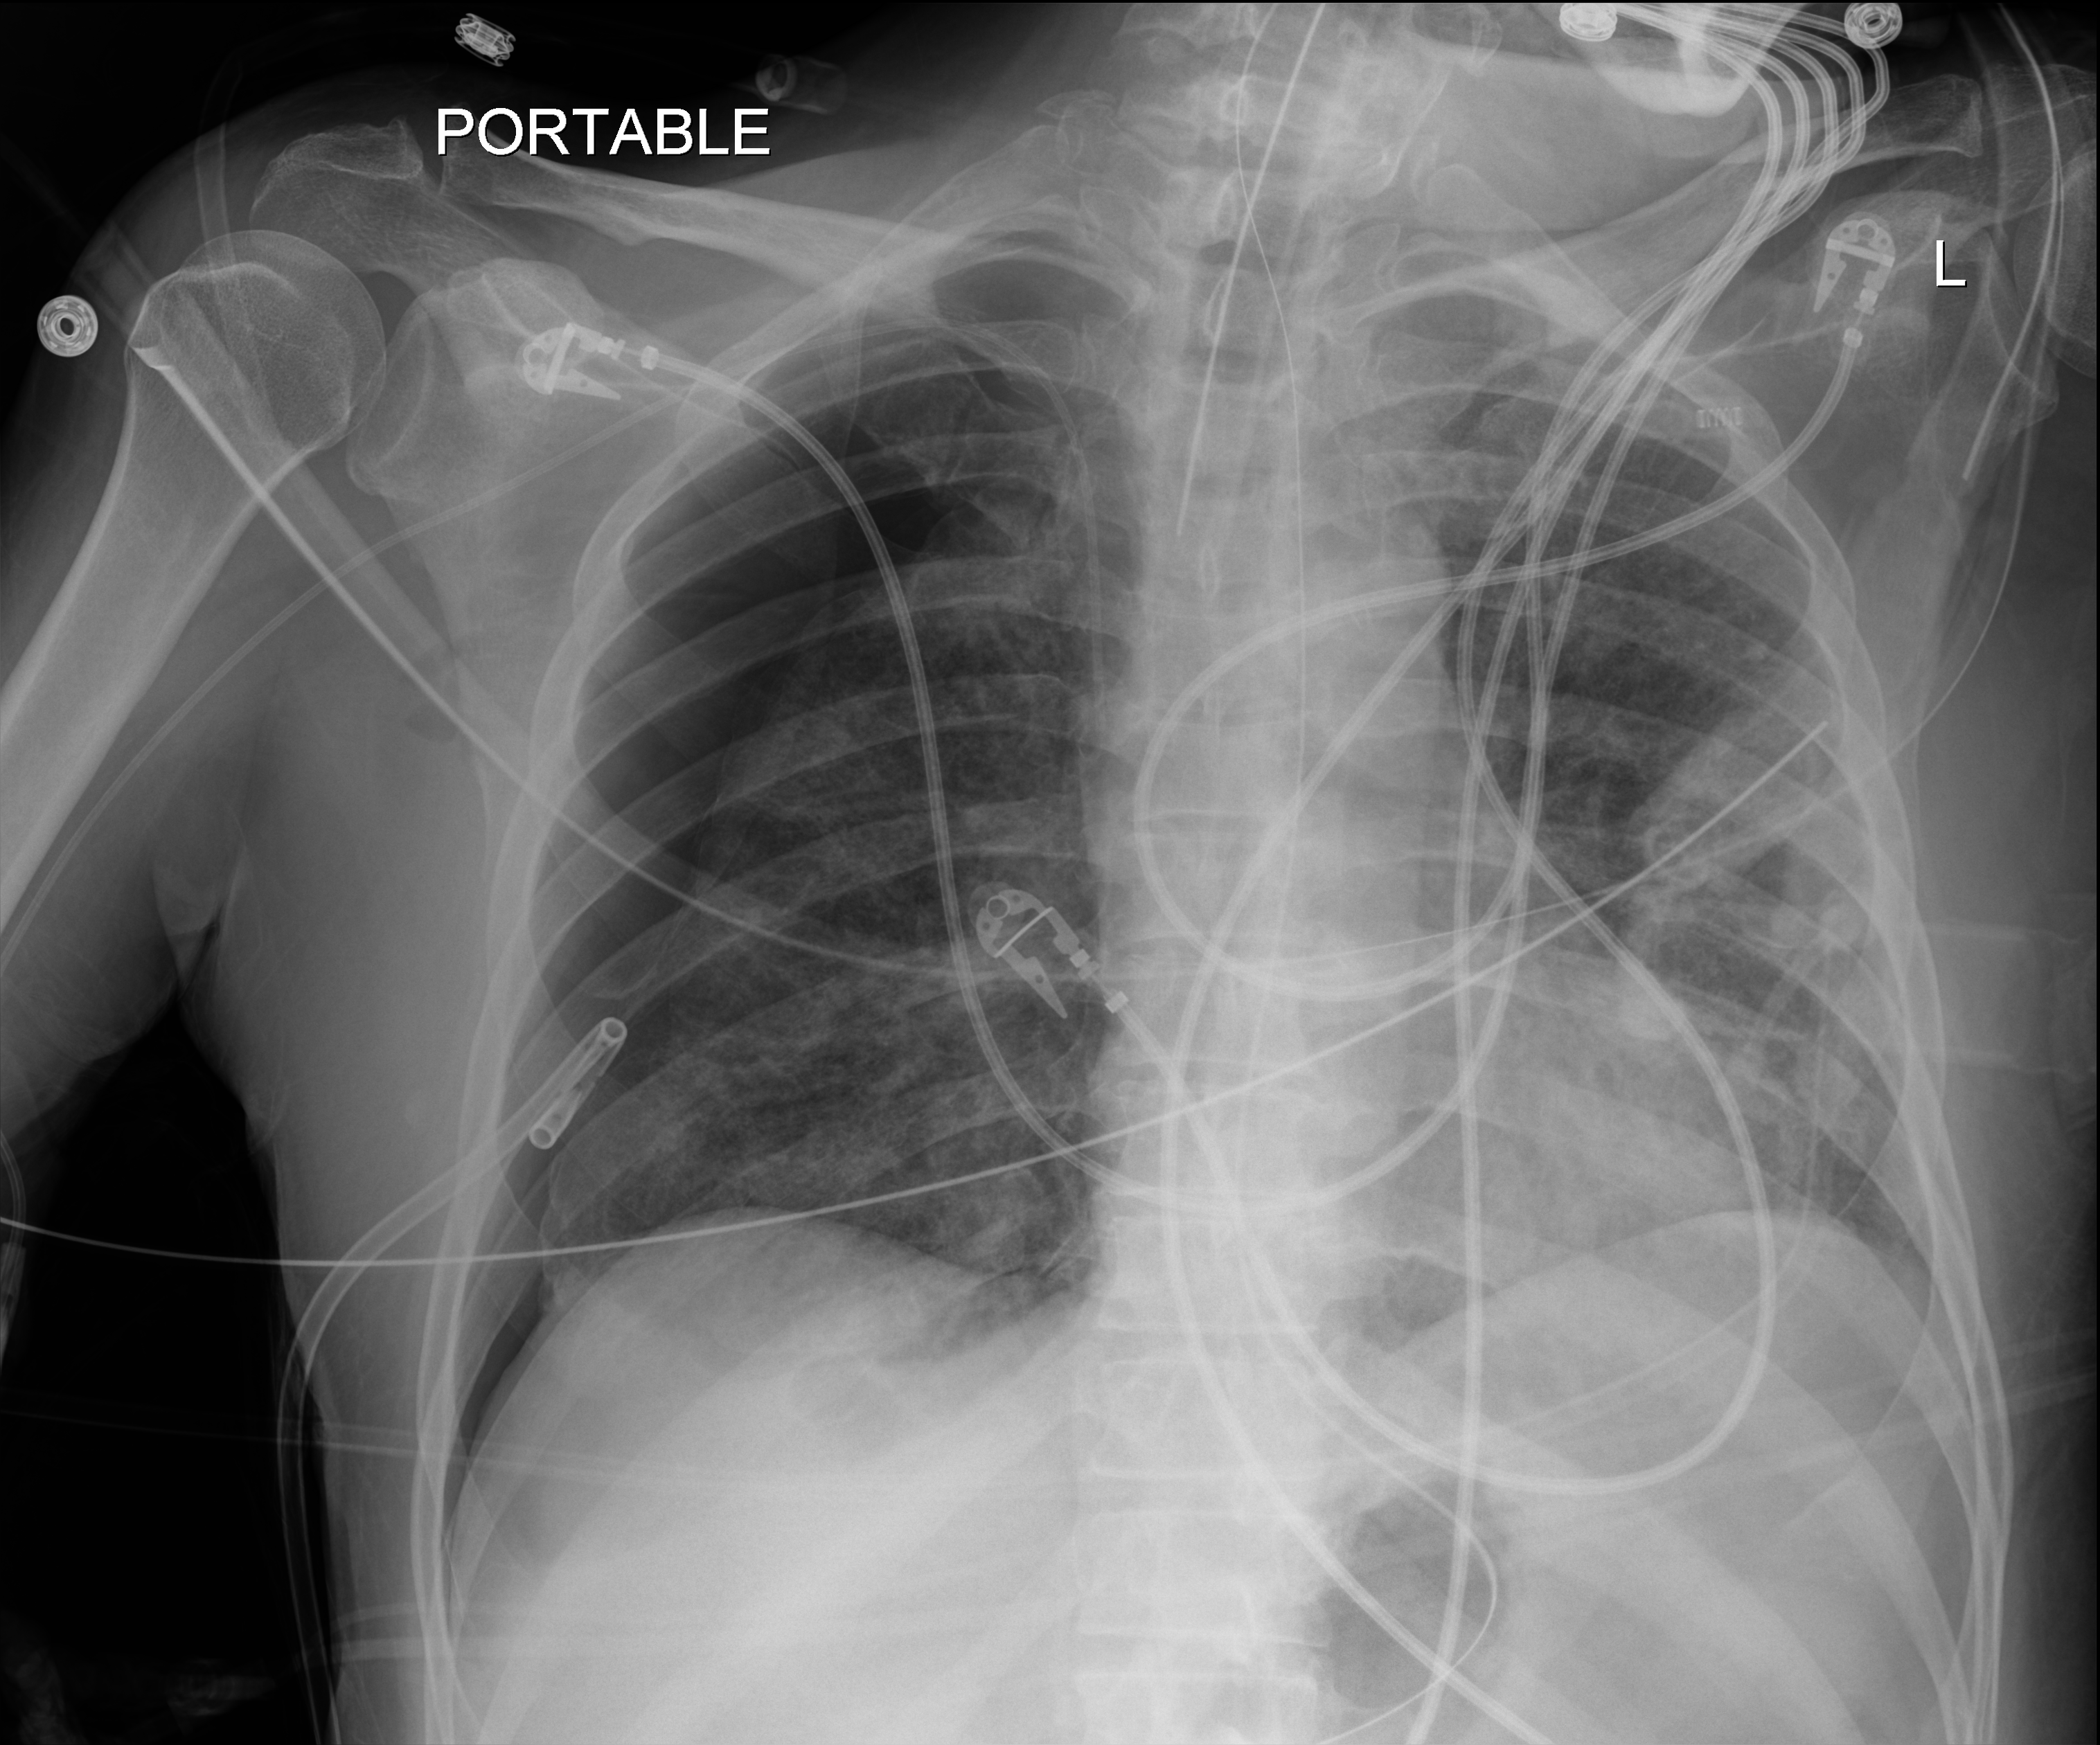
Chest X-ray (portable). Male patient hospitalised with COVID-19, age 18–59 years.
Hospital-stay facts (about this admission, not read from this image; timing relative to this image not recorded):
- mechanically ventilated during this hospital stay: yes